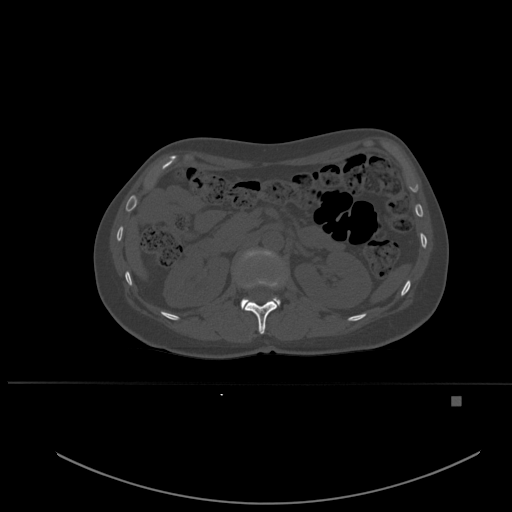
CT including the spine, one axial slice; slice 246 of 651 in the series (ordered by position); bone window (W 1800 / L 400 HU); 512 × 512 image matrix. Female patient, age 49 years. From the clinical record (not read from this slice): primary cancer: breast; vertebrae with lytic lesions (as recorded): L3, T12, L4.
Structures marked on this image (semi-automatic segmentation, software-assisted and operator-edited):
- L1 vertebra: bounding box <240,250,281,309> (left, top, right, bottom; pixels)
- T12 vertebra: <244,278,278,334>